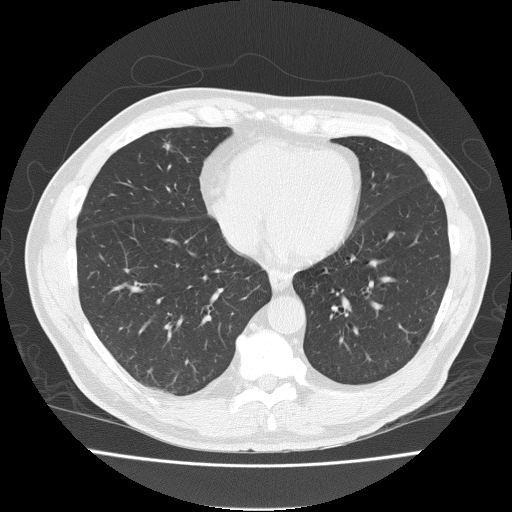
Chest CT (low-dose screening protocol), one axial image, baseline annual screen, lung window (W 1500 / L -600 HU), 2 mm slice thickness, lung (sharp) reconstruction kernel (FC51), 120 kVp, slice 126 of 191 in the series, 512 × 512 image matrix, field of view 375 × 375 mm. Male participant, aged 57 years at enrolment. Current smoker at enrolment.
Expert reader's lesion annotation, bounding box [x1, y1, x2, y2] px = [155, 133, 186, 167]. The exam's reader record, not a measurement of the box and not confirmed to be the same lesion: non-calcified nodule or mass ≥4 mm, right middle lobe, 4 × 4 mm, spiculated (stellate) margins, soft tissue attenuation. Later outcome: lung cancer diagnosed 459 days after this screen — adenocarcinoma, NOS, right middle lobe, moderately differentiated (G2), stage IA (AJCC 6th edition), 12 mm at pathology.